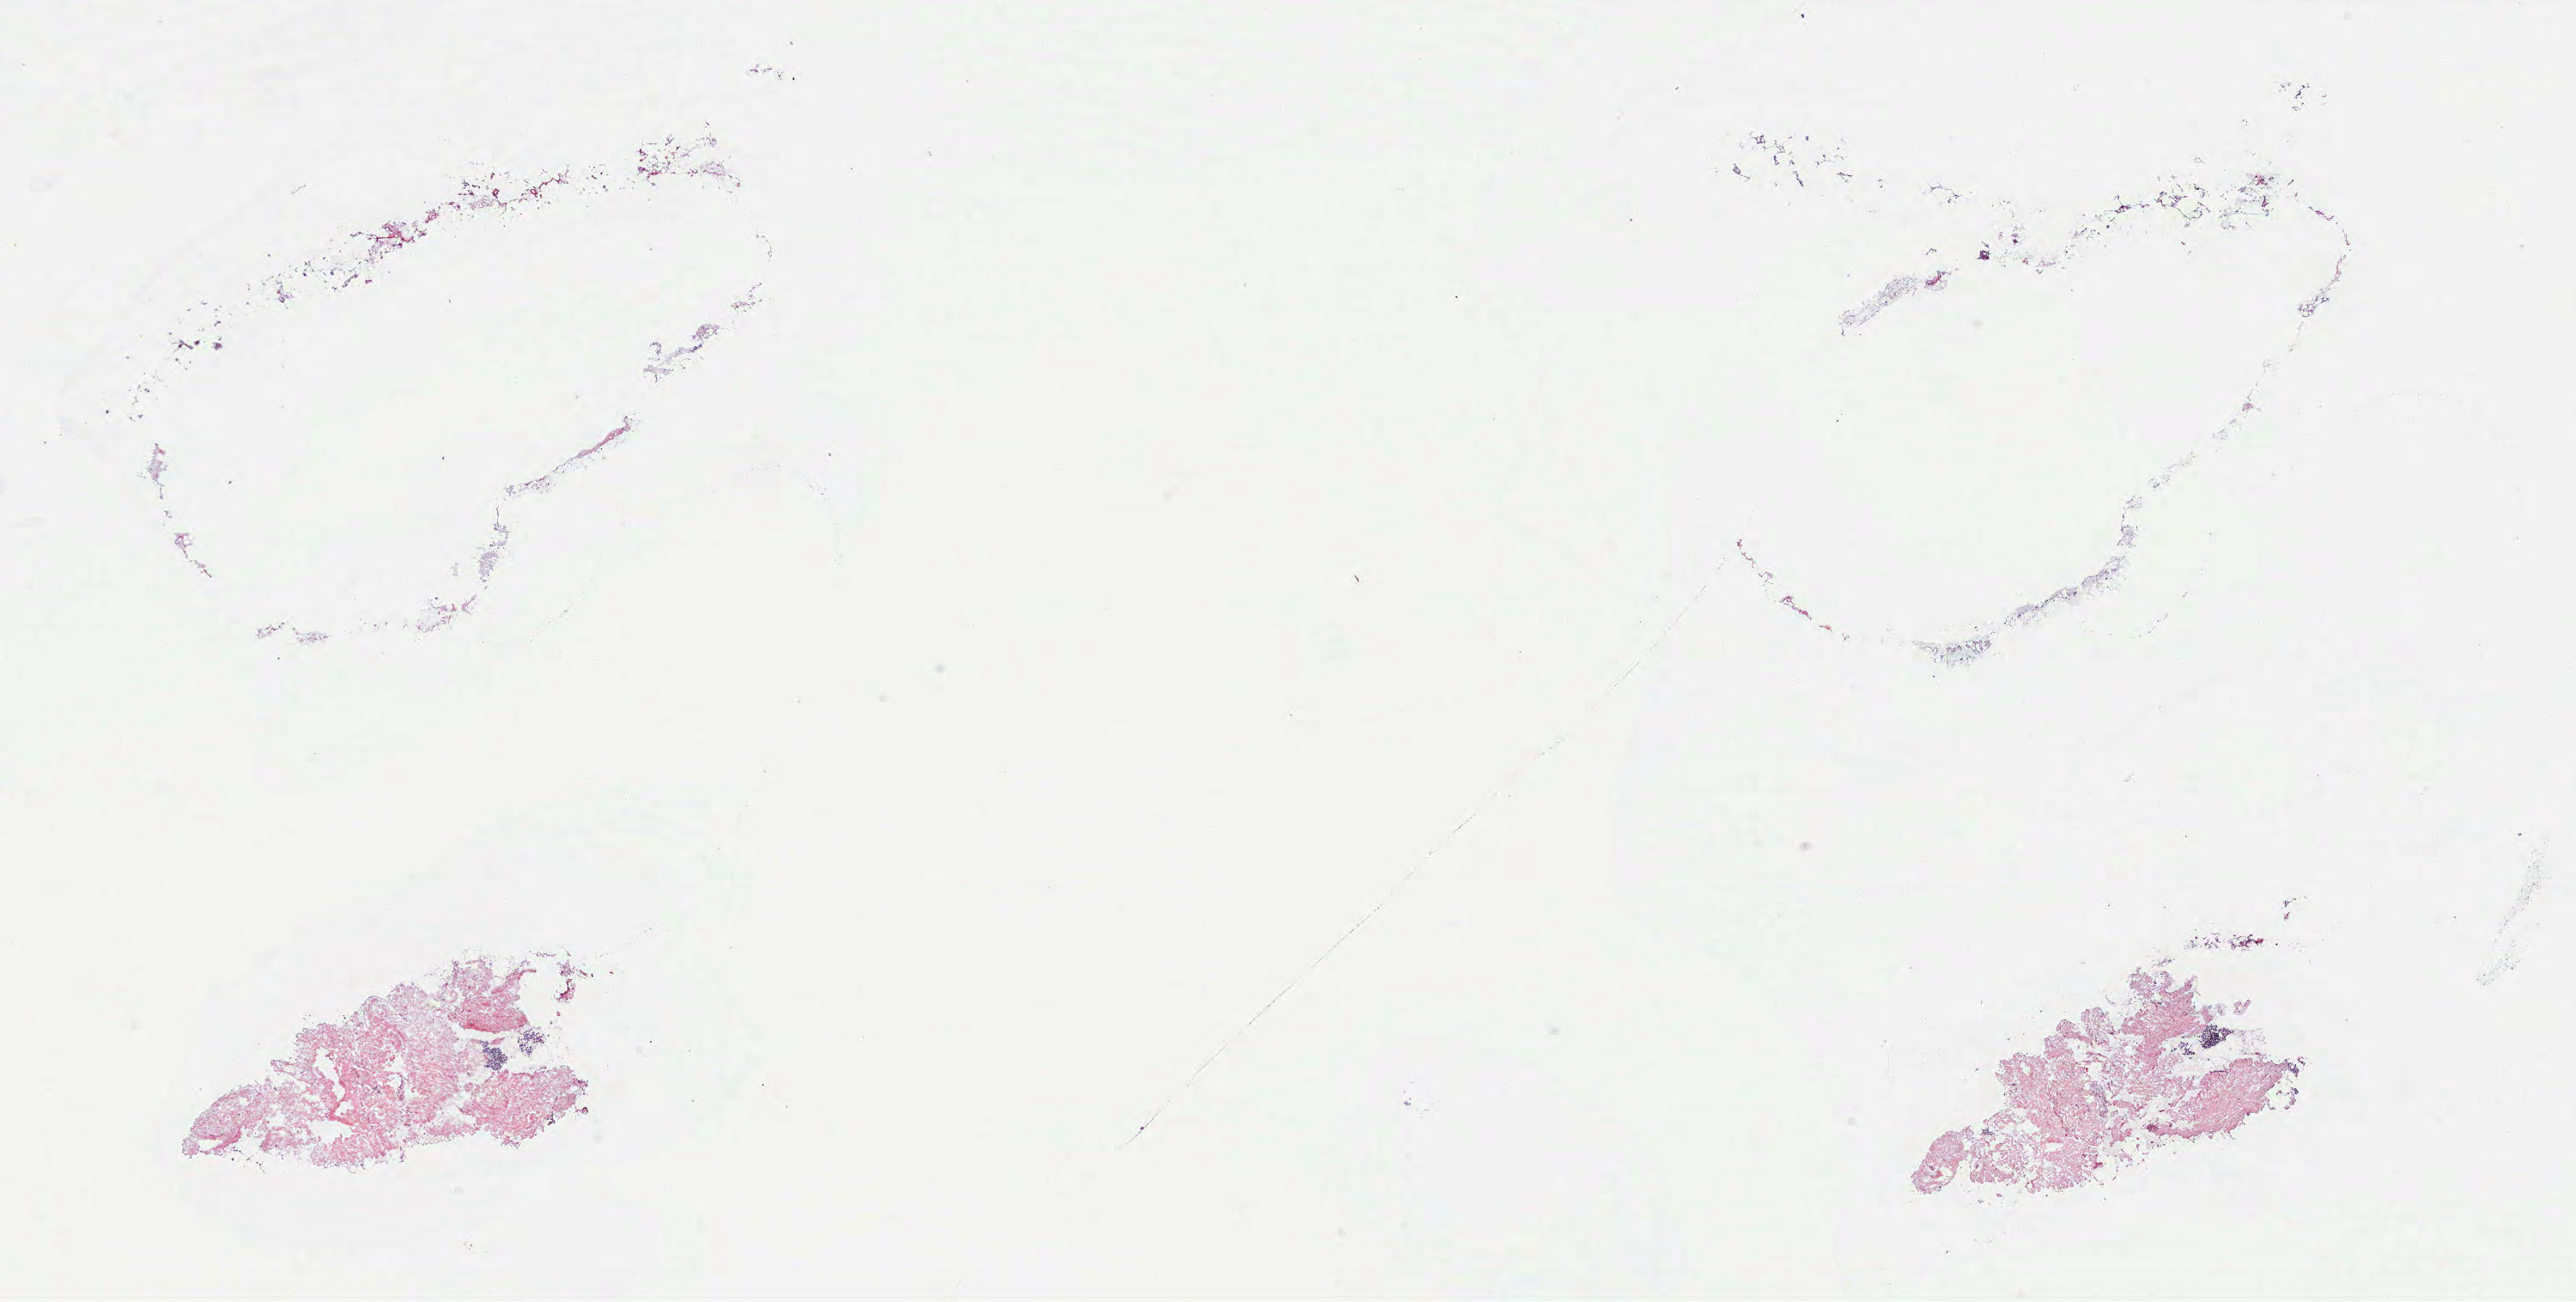
Digitized H&E-stained tissue section (whole slide) — a low-resolution overview of the entire scanned area, about 24.0 x 12.1 mm, breast, tissue type not recorded.
Patient diagnosis (cohort enrolment): breast cancer (breast).